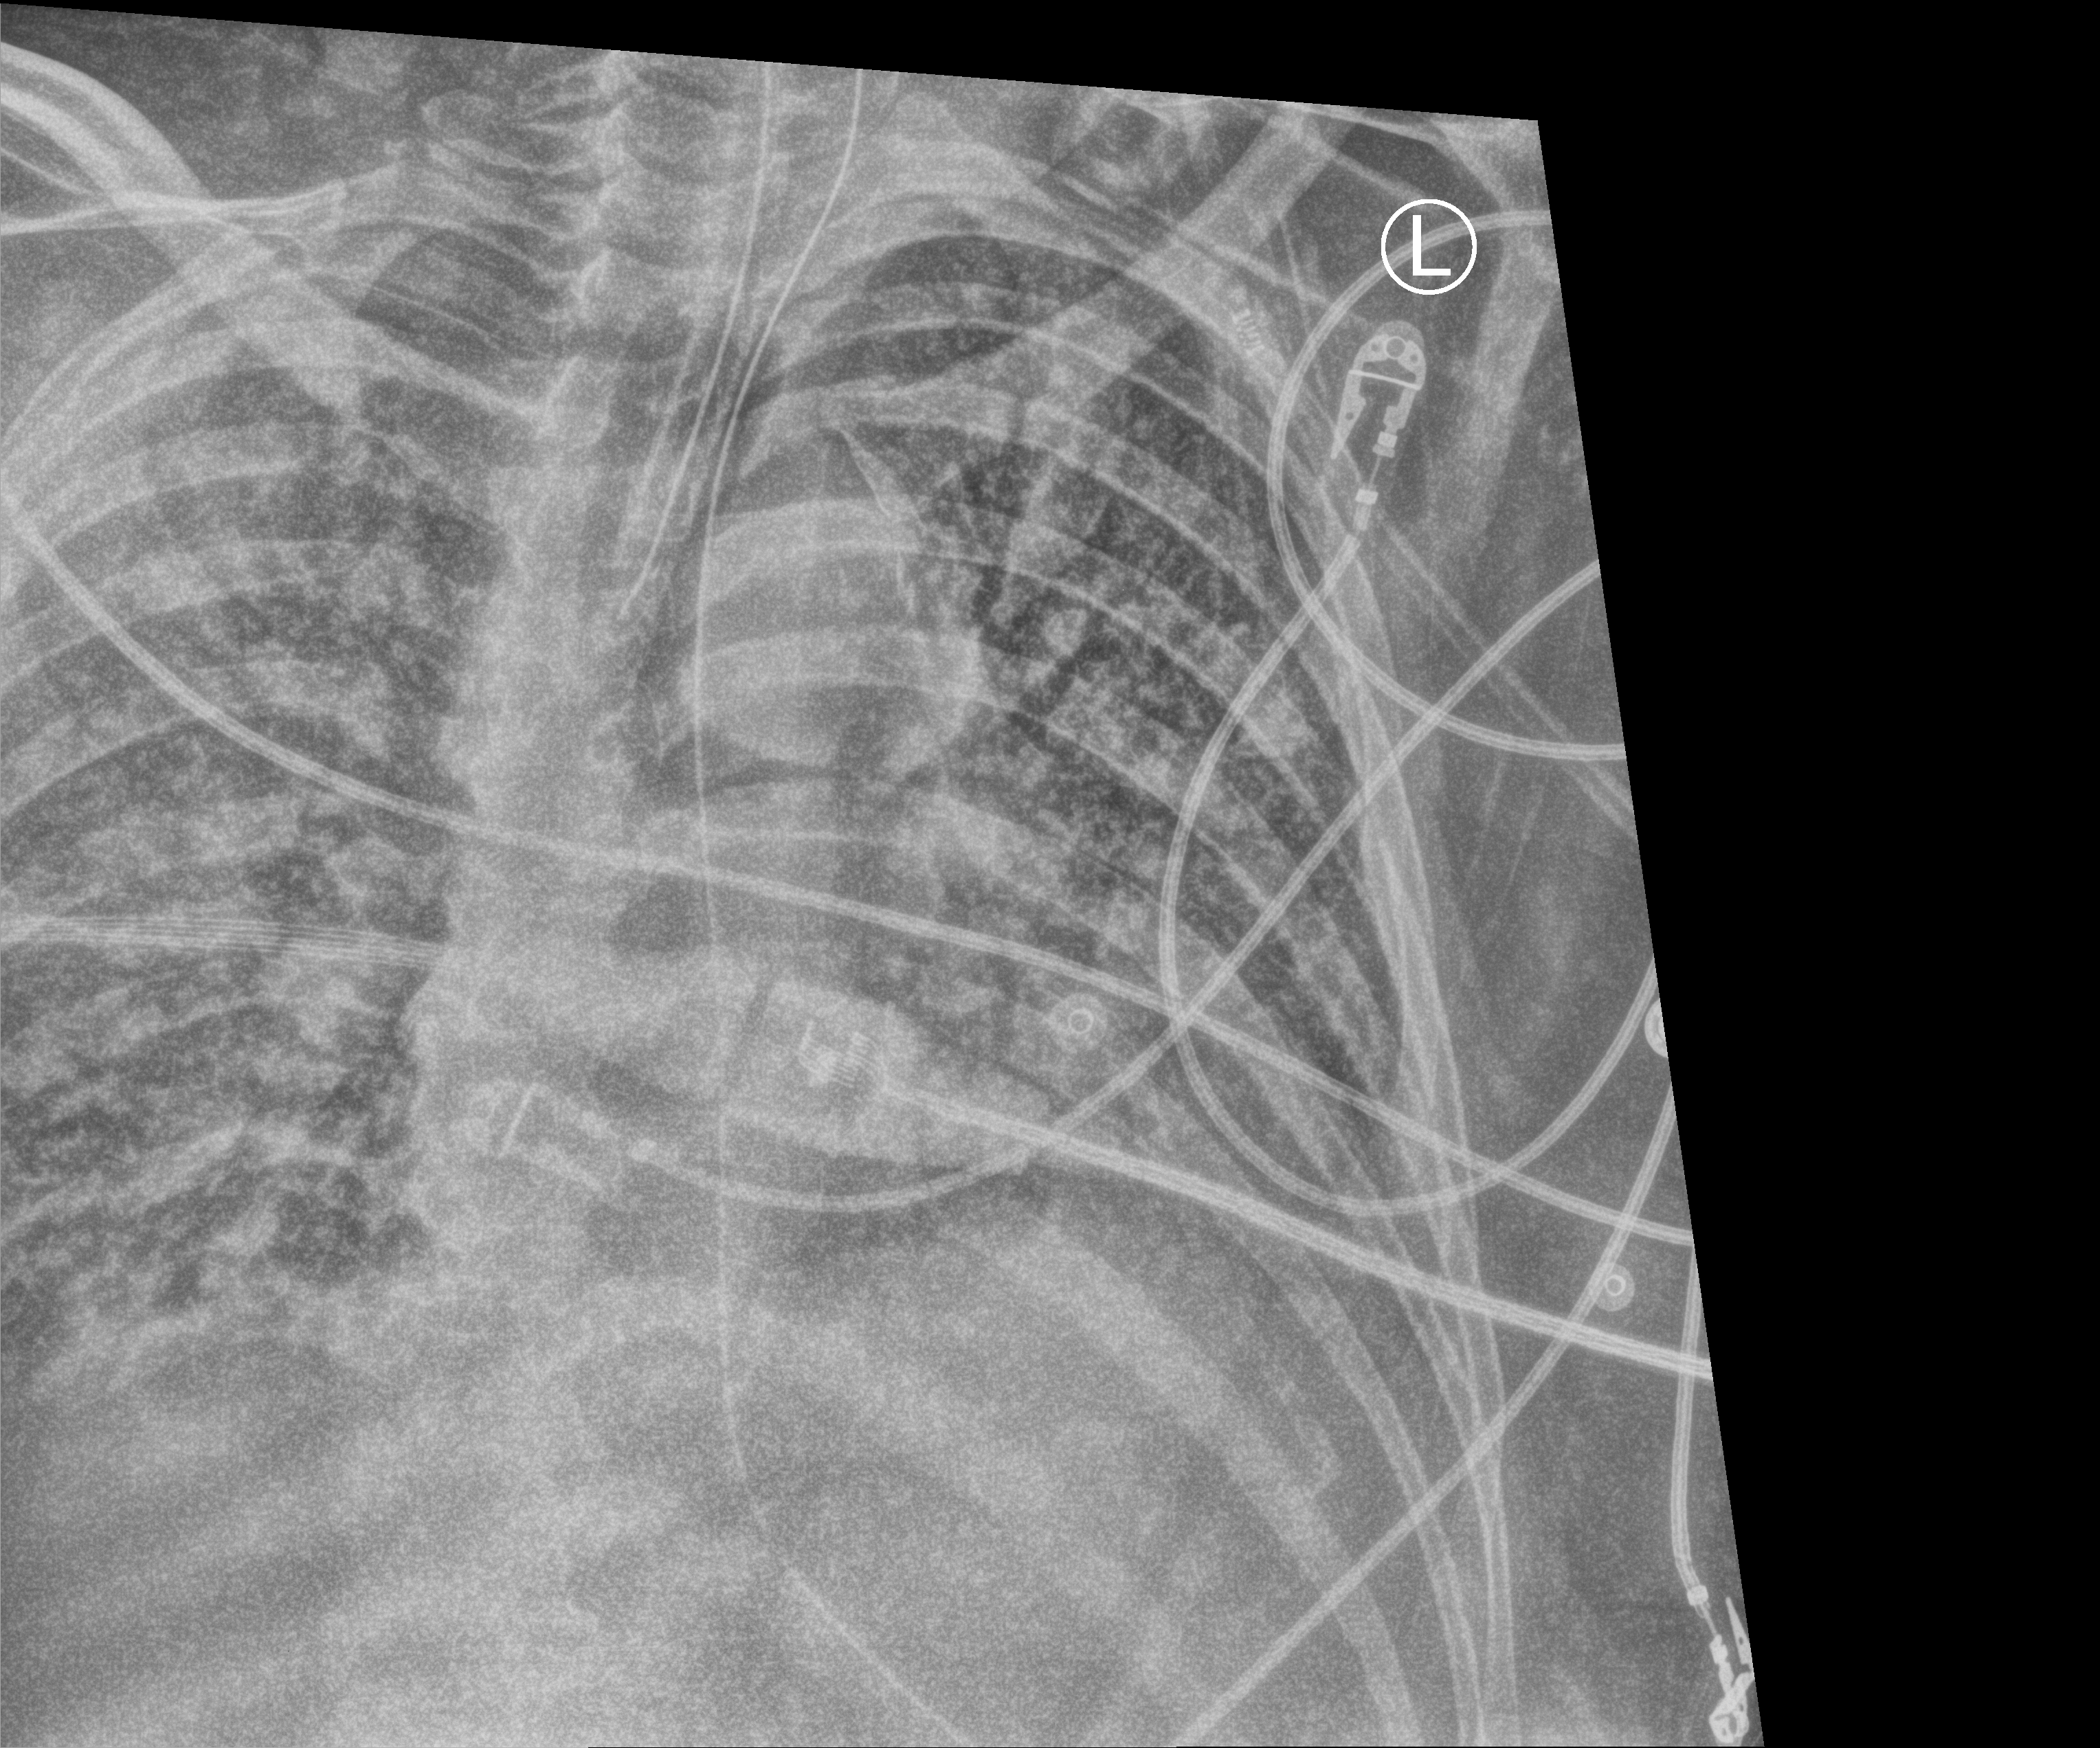
Chest X-ray (portable); anteroposterior (AP) projection. Patient hospitalised with COVID-19; male, aged 60–74 years.
Admission-level facts for this patient (not findings on this image; timing relative to this image not recorded):
- length of hospital stay: 40 days
- admitted to intensive care during this hospital stay: yes
- diabetes (admission record): no